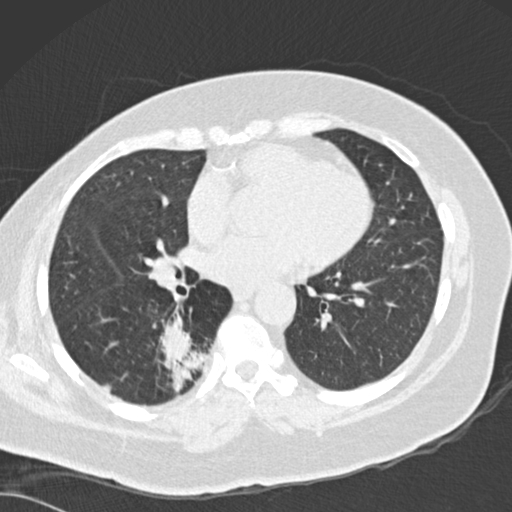
Low-dose screening chest CT, one axial slice. Slice 72 of 162 in the series (ordered by position). Reconstruction kernel B30f. 120 kVp. Lung window (W 1500 / L -600 HU). 2 mm slice thickness. 512 × 512 image matrix, field of view 328 × 328 mm.
Annotated regions visible in this slice (outlined manually by an expert reader):
- lesion 1 (tumor, lower lobe of right lung): bounding box (x1, y1, x2, y2) in pixels: (159, 321, 206, 394)